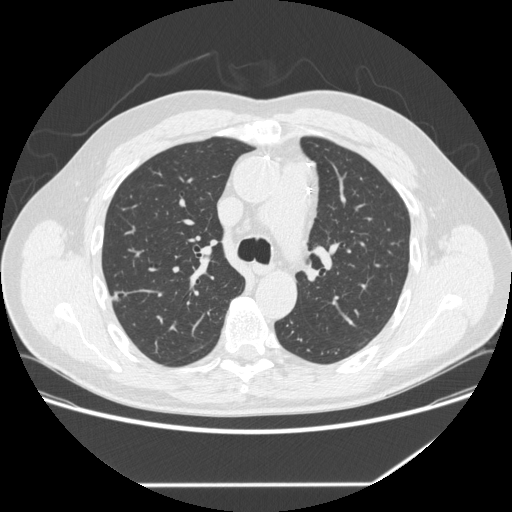
Chest CT (low-dose screening protocol), one axial image. First (baseline) screen. Lung window (W 1500 / L -600 HU). 1.25 mm slice thickness. Male participant, aged 62 years at enrolment. Current smoker at enrolment.
Expert-annotated lung lesion, bounding box (x1, y1, x2, y2) in pixels: (100, 281, 133, 312). Screening reader's record for this exam: no non-calcified nodule ≥4 mm recorded. Participant outcome: lung cancer diagnosed 839 days after this screen — adenocarcinoma, NOS, right upper lobe, moderately differentiated (G2), stage IA (AJCC 6th edition), 12 mm at pathology.